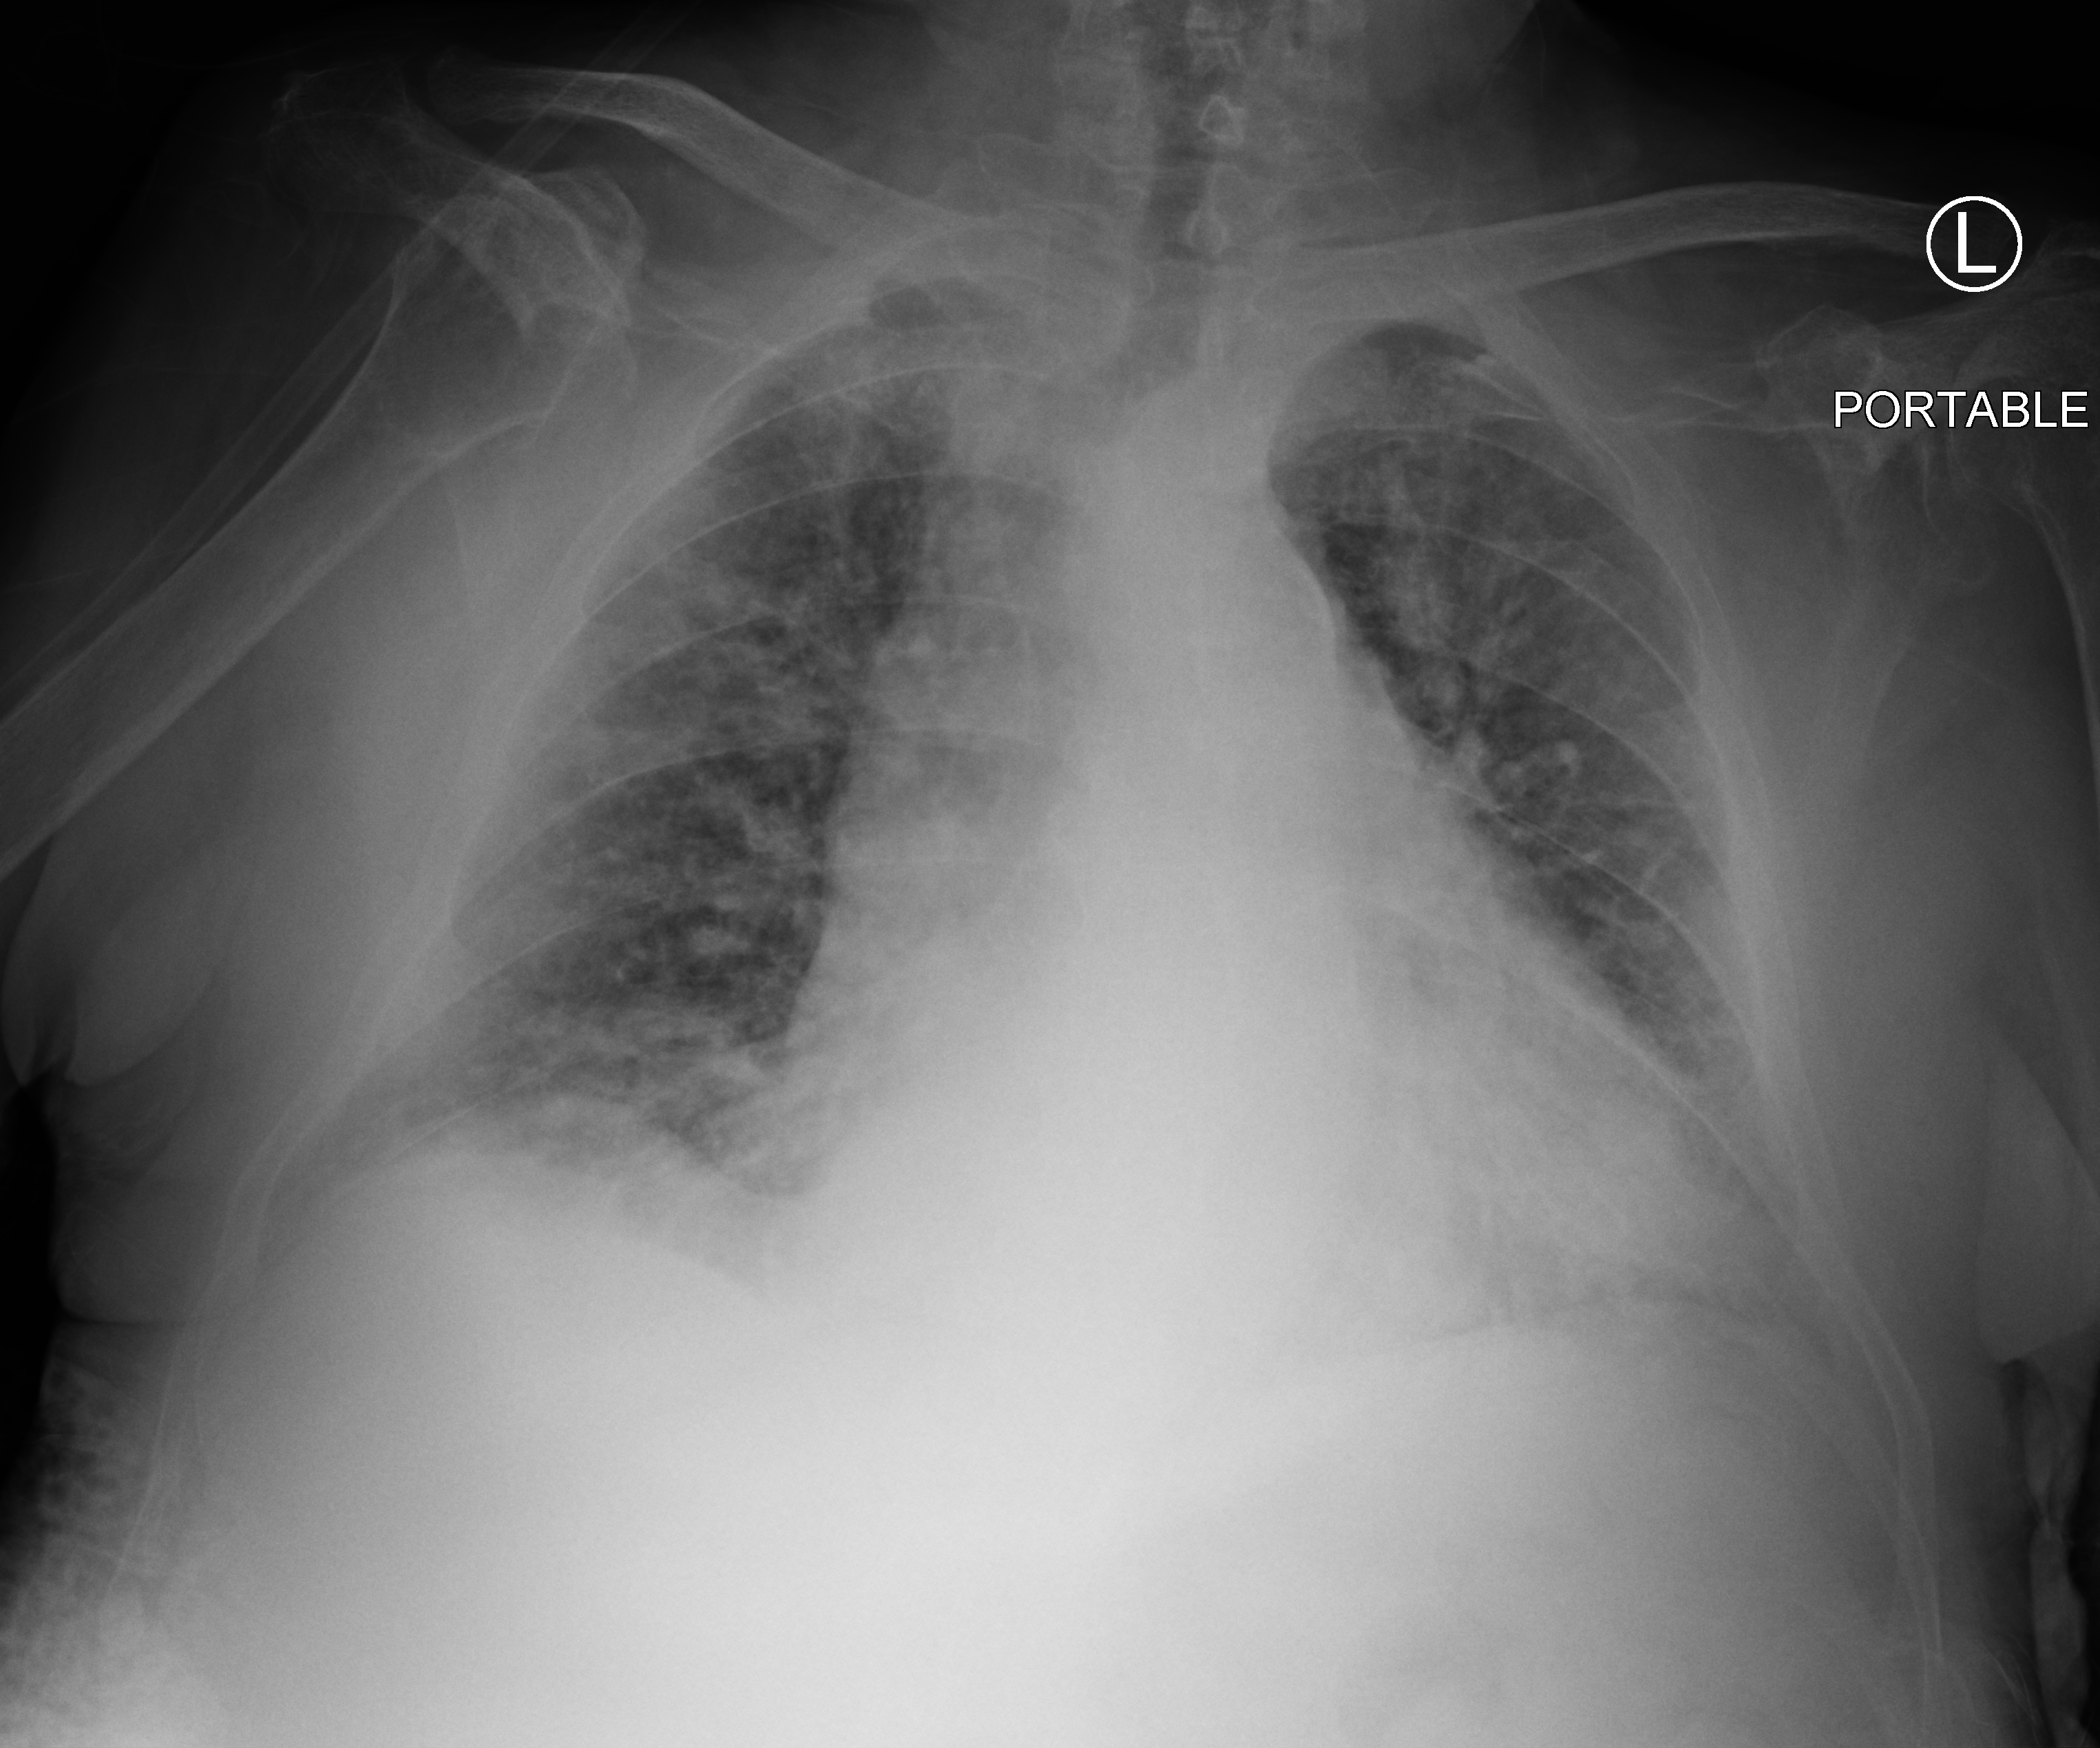
Portable chest radiograph. Male patient hospitalised with COVID-19, age 75–90 years.
Hospital-stay facts (about this admission, not read from this image; timing relative to this image not recorded): admitted to intensive care during this hospital stay: no; mechanically ventilated during this hospital stay: no.